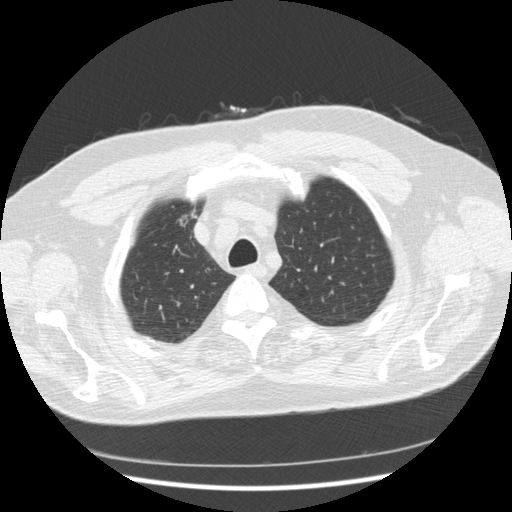
Axial slice from a low-dose chest CT screening exam; second screening round (one year after baseline); lung window (W 1500 / L -600 HU); standard (soft-tissue) reconstruction kernel (STANDARD); 120 kVp; slice 41 of 267 in the series. Male participant, aged 66 years at enrolment.
Expert-annotated lung lesion, bounding box (x1, y1, x2, y2) in pixels: (157, 202, 207, 241). Screening reader's record for this exam: no non-calcified nodule ≥4 mm recorded. Official screen result: positive, other. Lung cancer was diagnosed 603 days after this screen (after the third annual screen): bronchiolo-alveolar adenocarcinoma, NOS, right upper lobe, moderately differentiated (G2), stage IA (AJCC 6th edition), 12 mm at pathology.